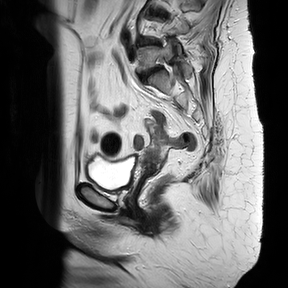
Pelvic MRI for cervical cancer, one sagittal slice; slice 16 of 37 in the series (ordered by position); T2-weighted; 1.5 T; TE 100 ms, TR 4174.1 ms; 4 mm slice thickness; 288 × 288 image matrix. Patient: female, 65 years.
Outlined on this slice (manually delineated by an expert):
- uterus and cervix: bounding box <141,126,164,169> (left, top, right, bottom; pixels)